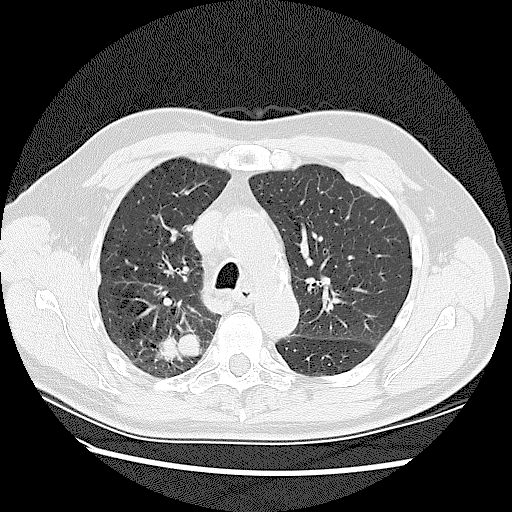
Low-dose screening chest CT, one axial slice; position 89 of 128 along the scan axis; lung window (W 1500 / L -600 HU); 2.5 mm slice thickness; 512 × 512 image matrix, field of view 360 × 360 mm.
Structures marked on this image (outlined manually by an expert reader):
- lesion 2 (tumor, upper lobe of right lung): bounding box [x1, y1, x2, y2] px = [162, 333, 201, 358]